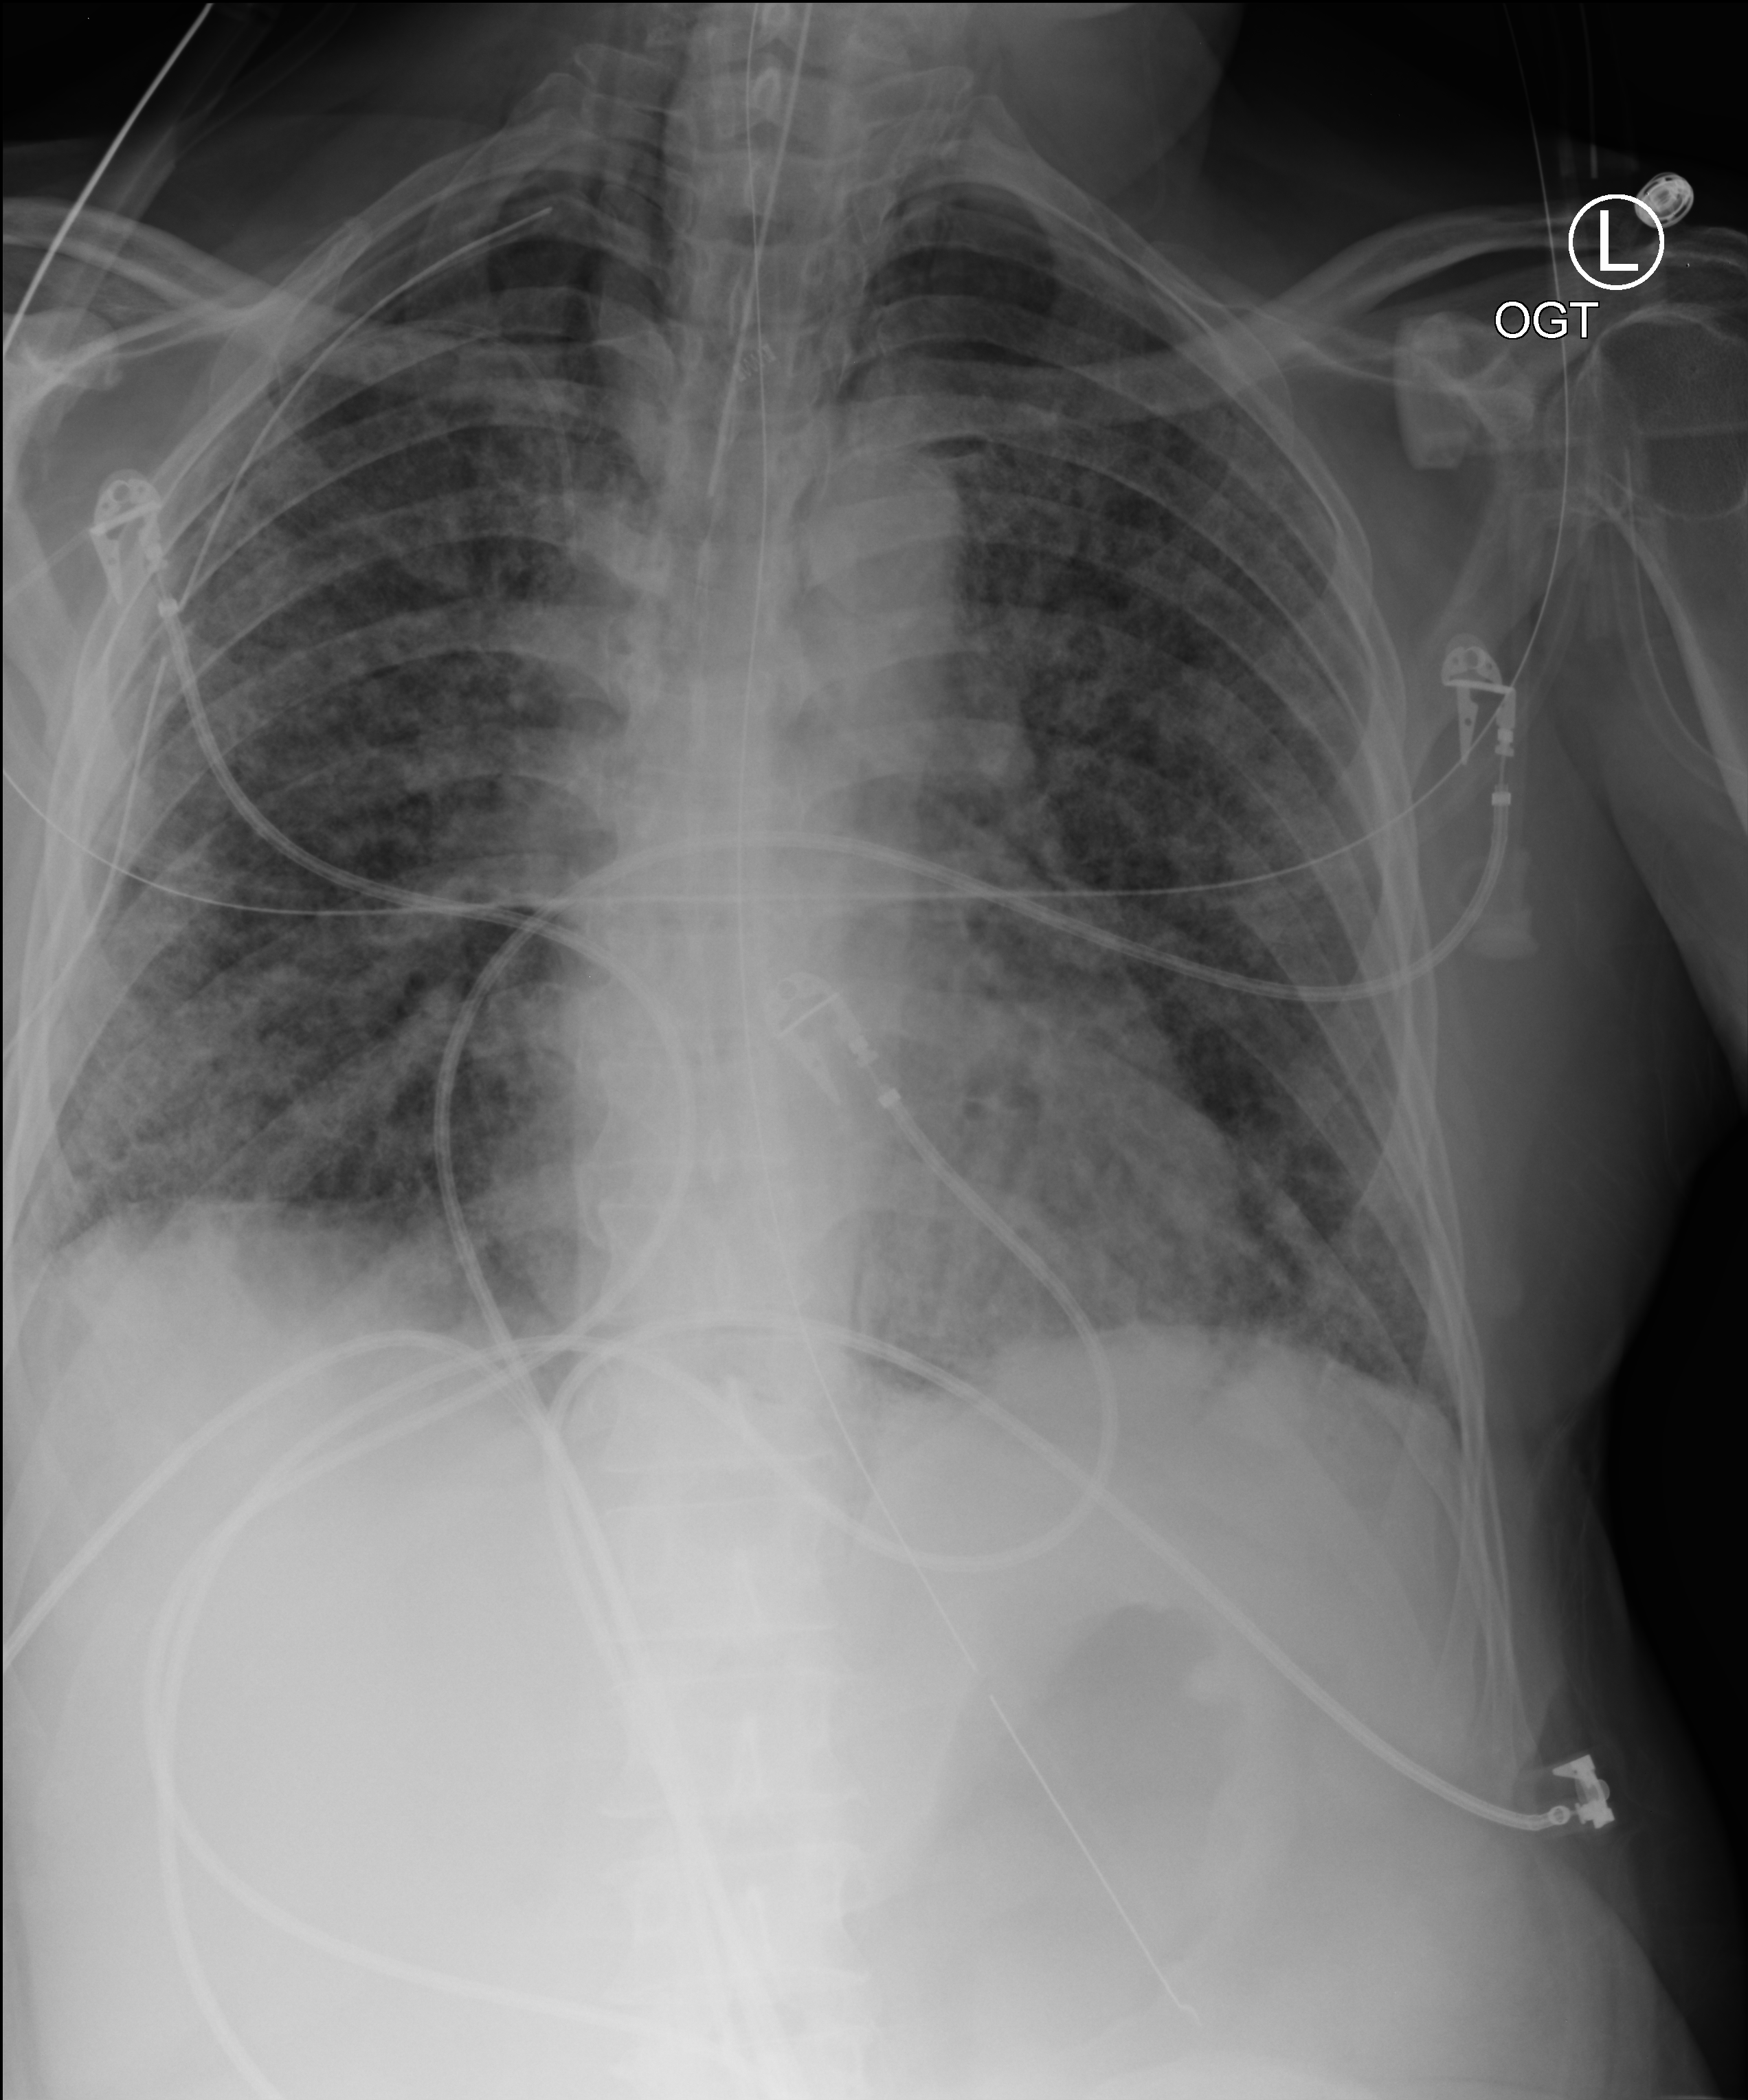
Bedside chest radiograph (computed radiography); anteroposterior (AP) projection. Patient hospitalised with COVID-19; male, aged 60–74 years.
Admission-level facts for this patient (not findings on this image; timing relative to this image not recorded):
- admitted to intensive care during this hospital stay: yes
- hypertension (admission record): no